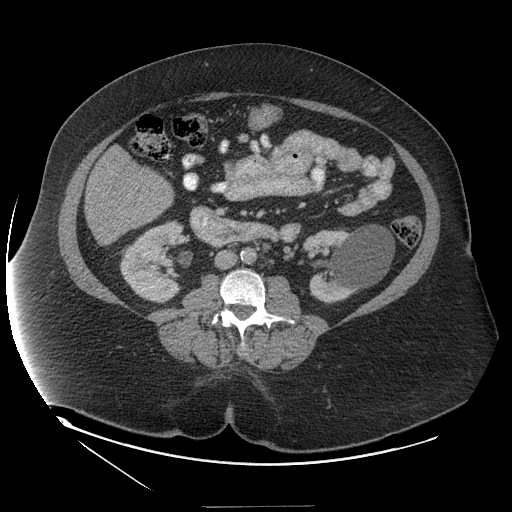
Contrast-enhanced abdominal CT (liver protocol), one axial slice; soft-tissue window (W 400 / L 40 HU); 512 × 512 image matrix, field of view 480 × 480 mm. Case-level facts recorded for this patient, not image findings: diagnosis: hepatocellular carcinoma (patient treated with transarterial chemoembolisation; whether this scan precedes or follows treatment is not stated here); TNM stage (as recorded): Stage-II; Child-Pugh class: A; tumour differentiation: well differentiated; tumour nodularity: multinodular.
Annotated regions visible in this slice (semi-automatic segmentation, software-assisted and operator-edited):
- liver parenchyma outside the tumour (the mass and vessels are separate outlines, so this box may not span the whole liver): bounding box [x1, y1, x2, y2] px = [84, 178, 172, 244]